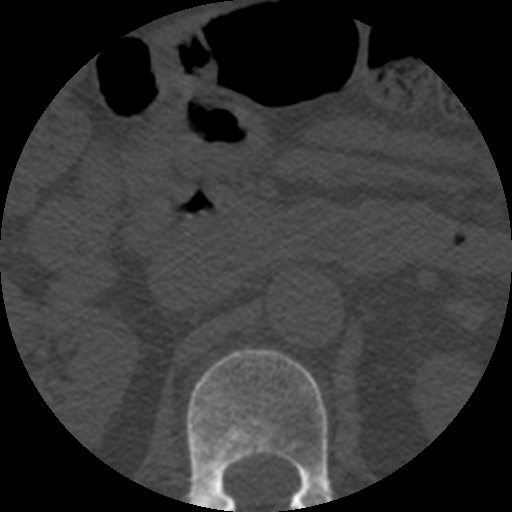
CT including the spine, one axial slice; slice 189 of 508 in the series (ordered by position); 120 kVp; bone window (W 1800 / L 400 HU); 1.25 mm slice thickness; 512 × 512 image matrix, field of view 160 × 160 mm. Patient age 57 years. From the clinical record (not read from this slice): primary cancer: prostate.
Outlined on this slice (semi-automatic segmentation, software-assisted and operator-edited):
- L1 vertebra: bounding box [x1, y1, x2, y2] px = [185, 349, 333, 512]